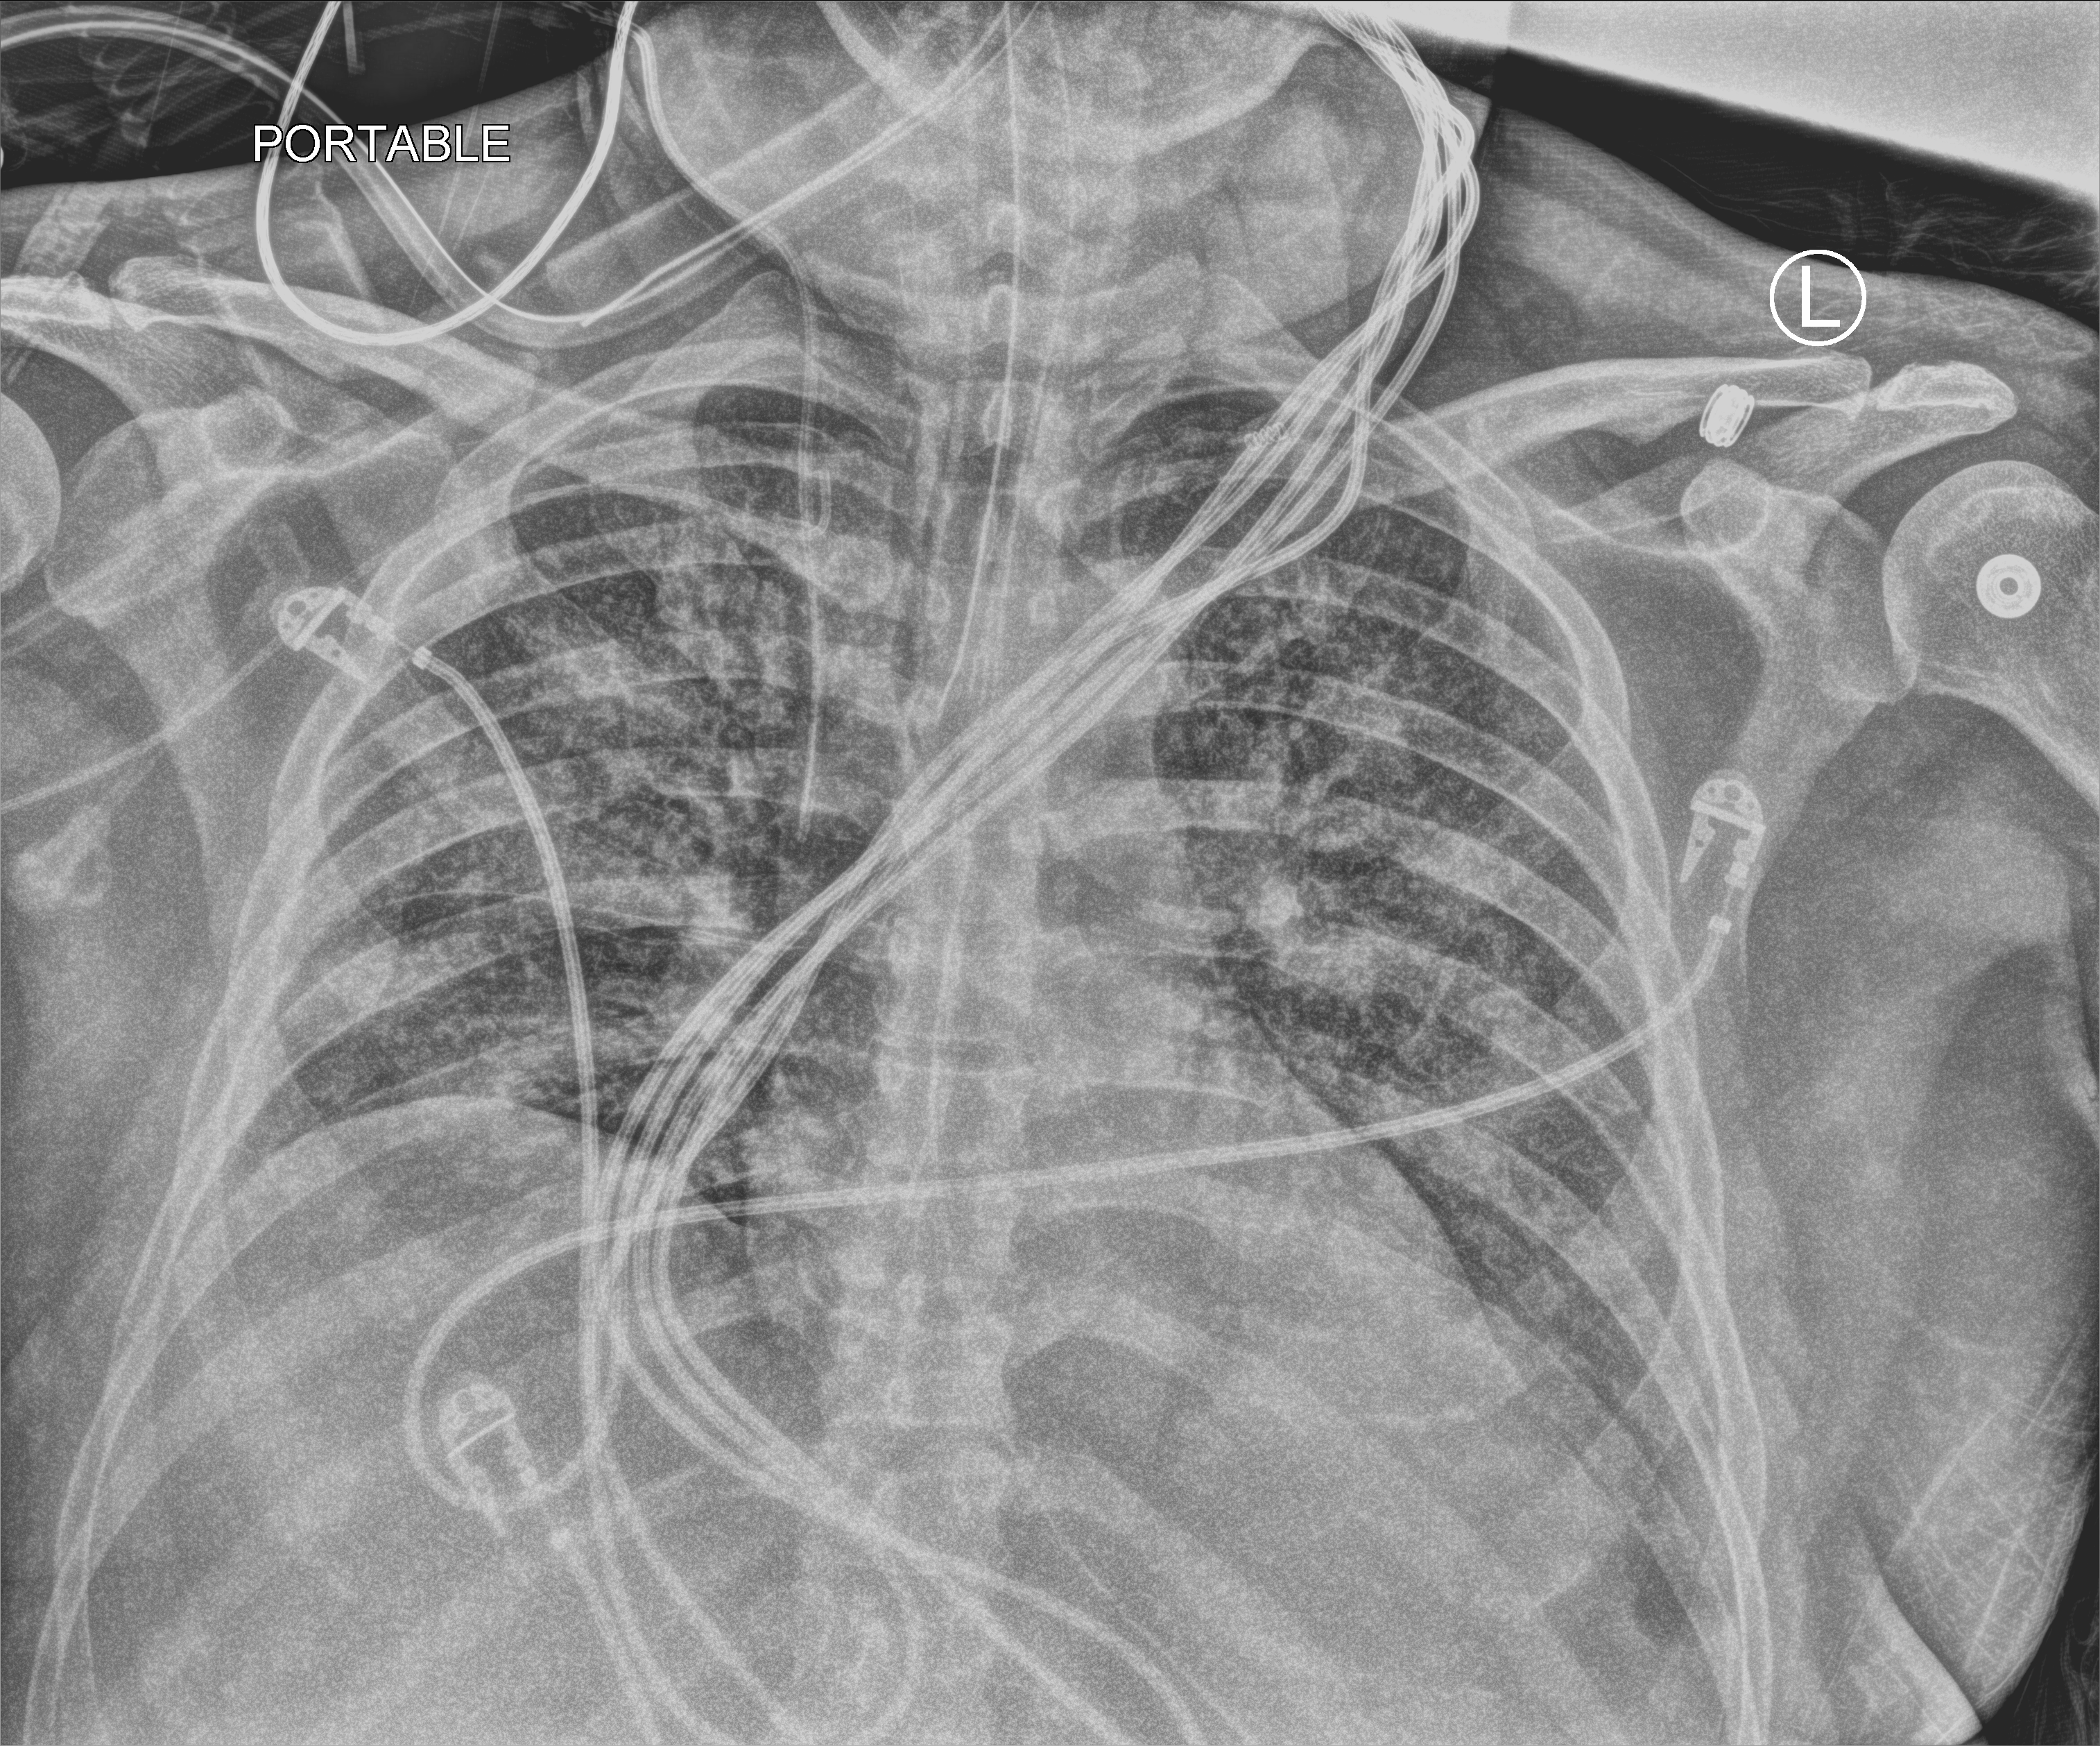
Portable chest radiograph, anteroposterior (AP) projection. Patient hospitalised with COVID-19; male, aged 18–59 years.
Admission-level facts for this patient (not findings on this image; timing relative to this image not recorded):
- COPD (admission record): no
- mechanically ventilated during this hospital stay: yes